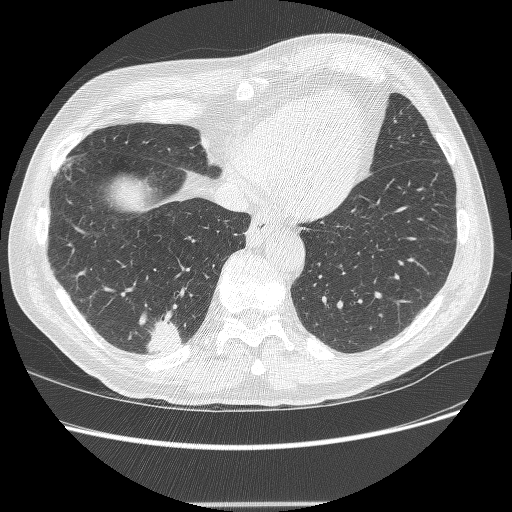
Low-dose screening chest CT, axial slice. Second screening round (one year after baseline). Lung window (W 1500 / L -600 HU). Lung (sharp) reconstruction kernel (BONE). Slice 64 of 245 in the series. 512 × 512 image matrix. Male participant, aged 71 years at enrolment.
• Expert reader's lesion annotation, bounding box <137,322,187,360> (left, top, right, bottom; pixels).
• The screening reader recorded 5 non-calcified nodules or masses ≥4 mm on this exam (right lower lobe, right lower lobe, right upper lobe, right upper lobe, right upper lobe); which of them this box marks is not recorded.
• Official screen result: positive, change unspecified: nodule(s) >= 4 mm or enlarging nodule(s), mass(es), or other non-specific abnormalities suspicious for lung cancer.
• Participant outcome: lung cancer diagnosed 7 days after this screen — squamous cell carcinoma, NOS, right lower lobe, moderately differentiated (G2), stage IA (AJCC 6th edition), 27 mm at pathology.